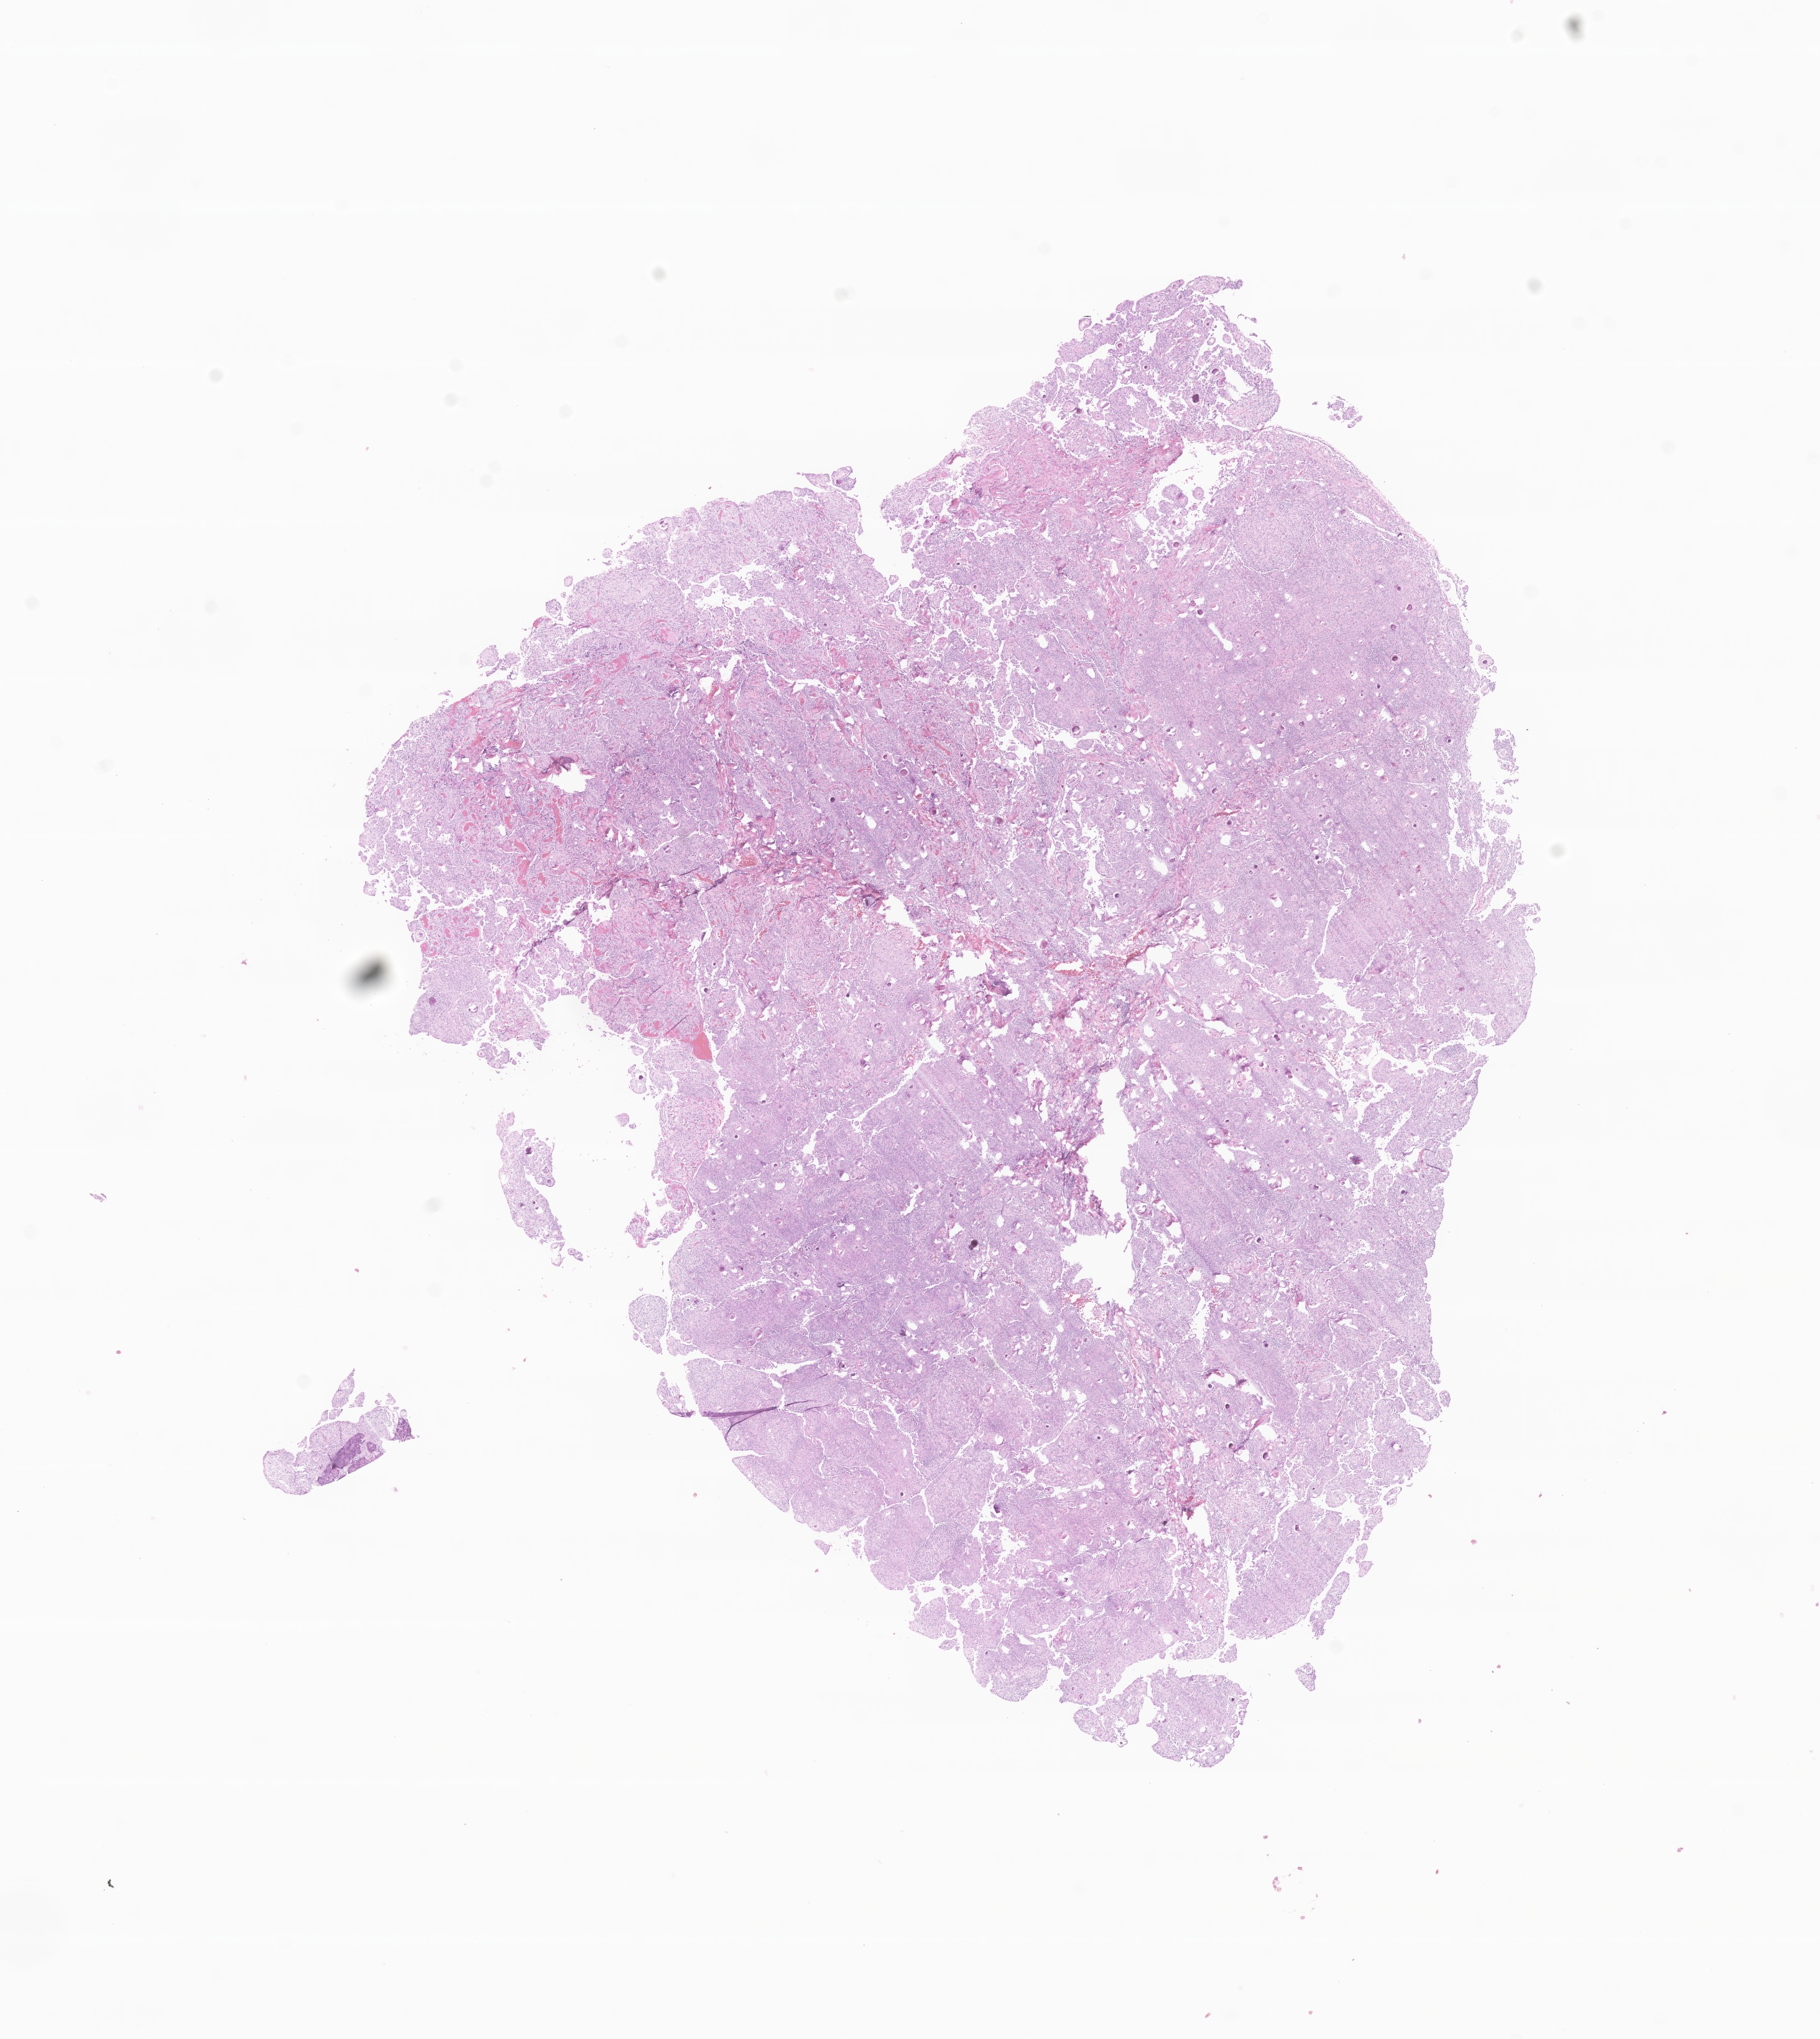
Whole-slide image, haematoxylin and eosin stain of tumor tissue from the spinal cord — whole scanned area (about 12.3 x 13.8 mm) shown as a low-resolution overview, FFPE section. Male patient, age 109 months (9 years 1 month).
Recorded diagnosis: Meningioma, NOS.